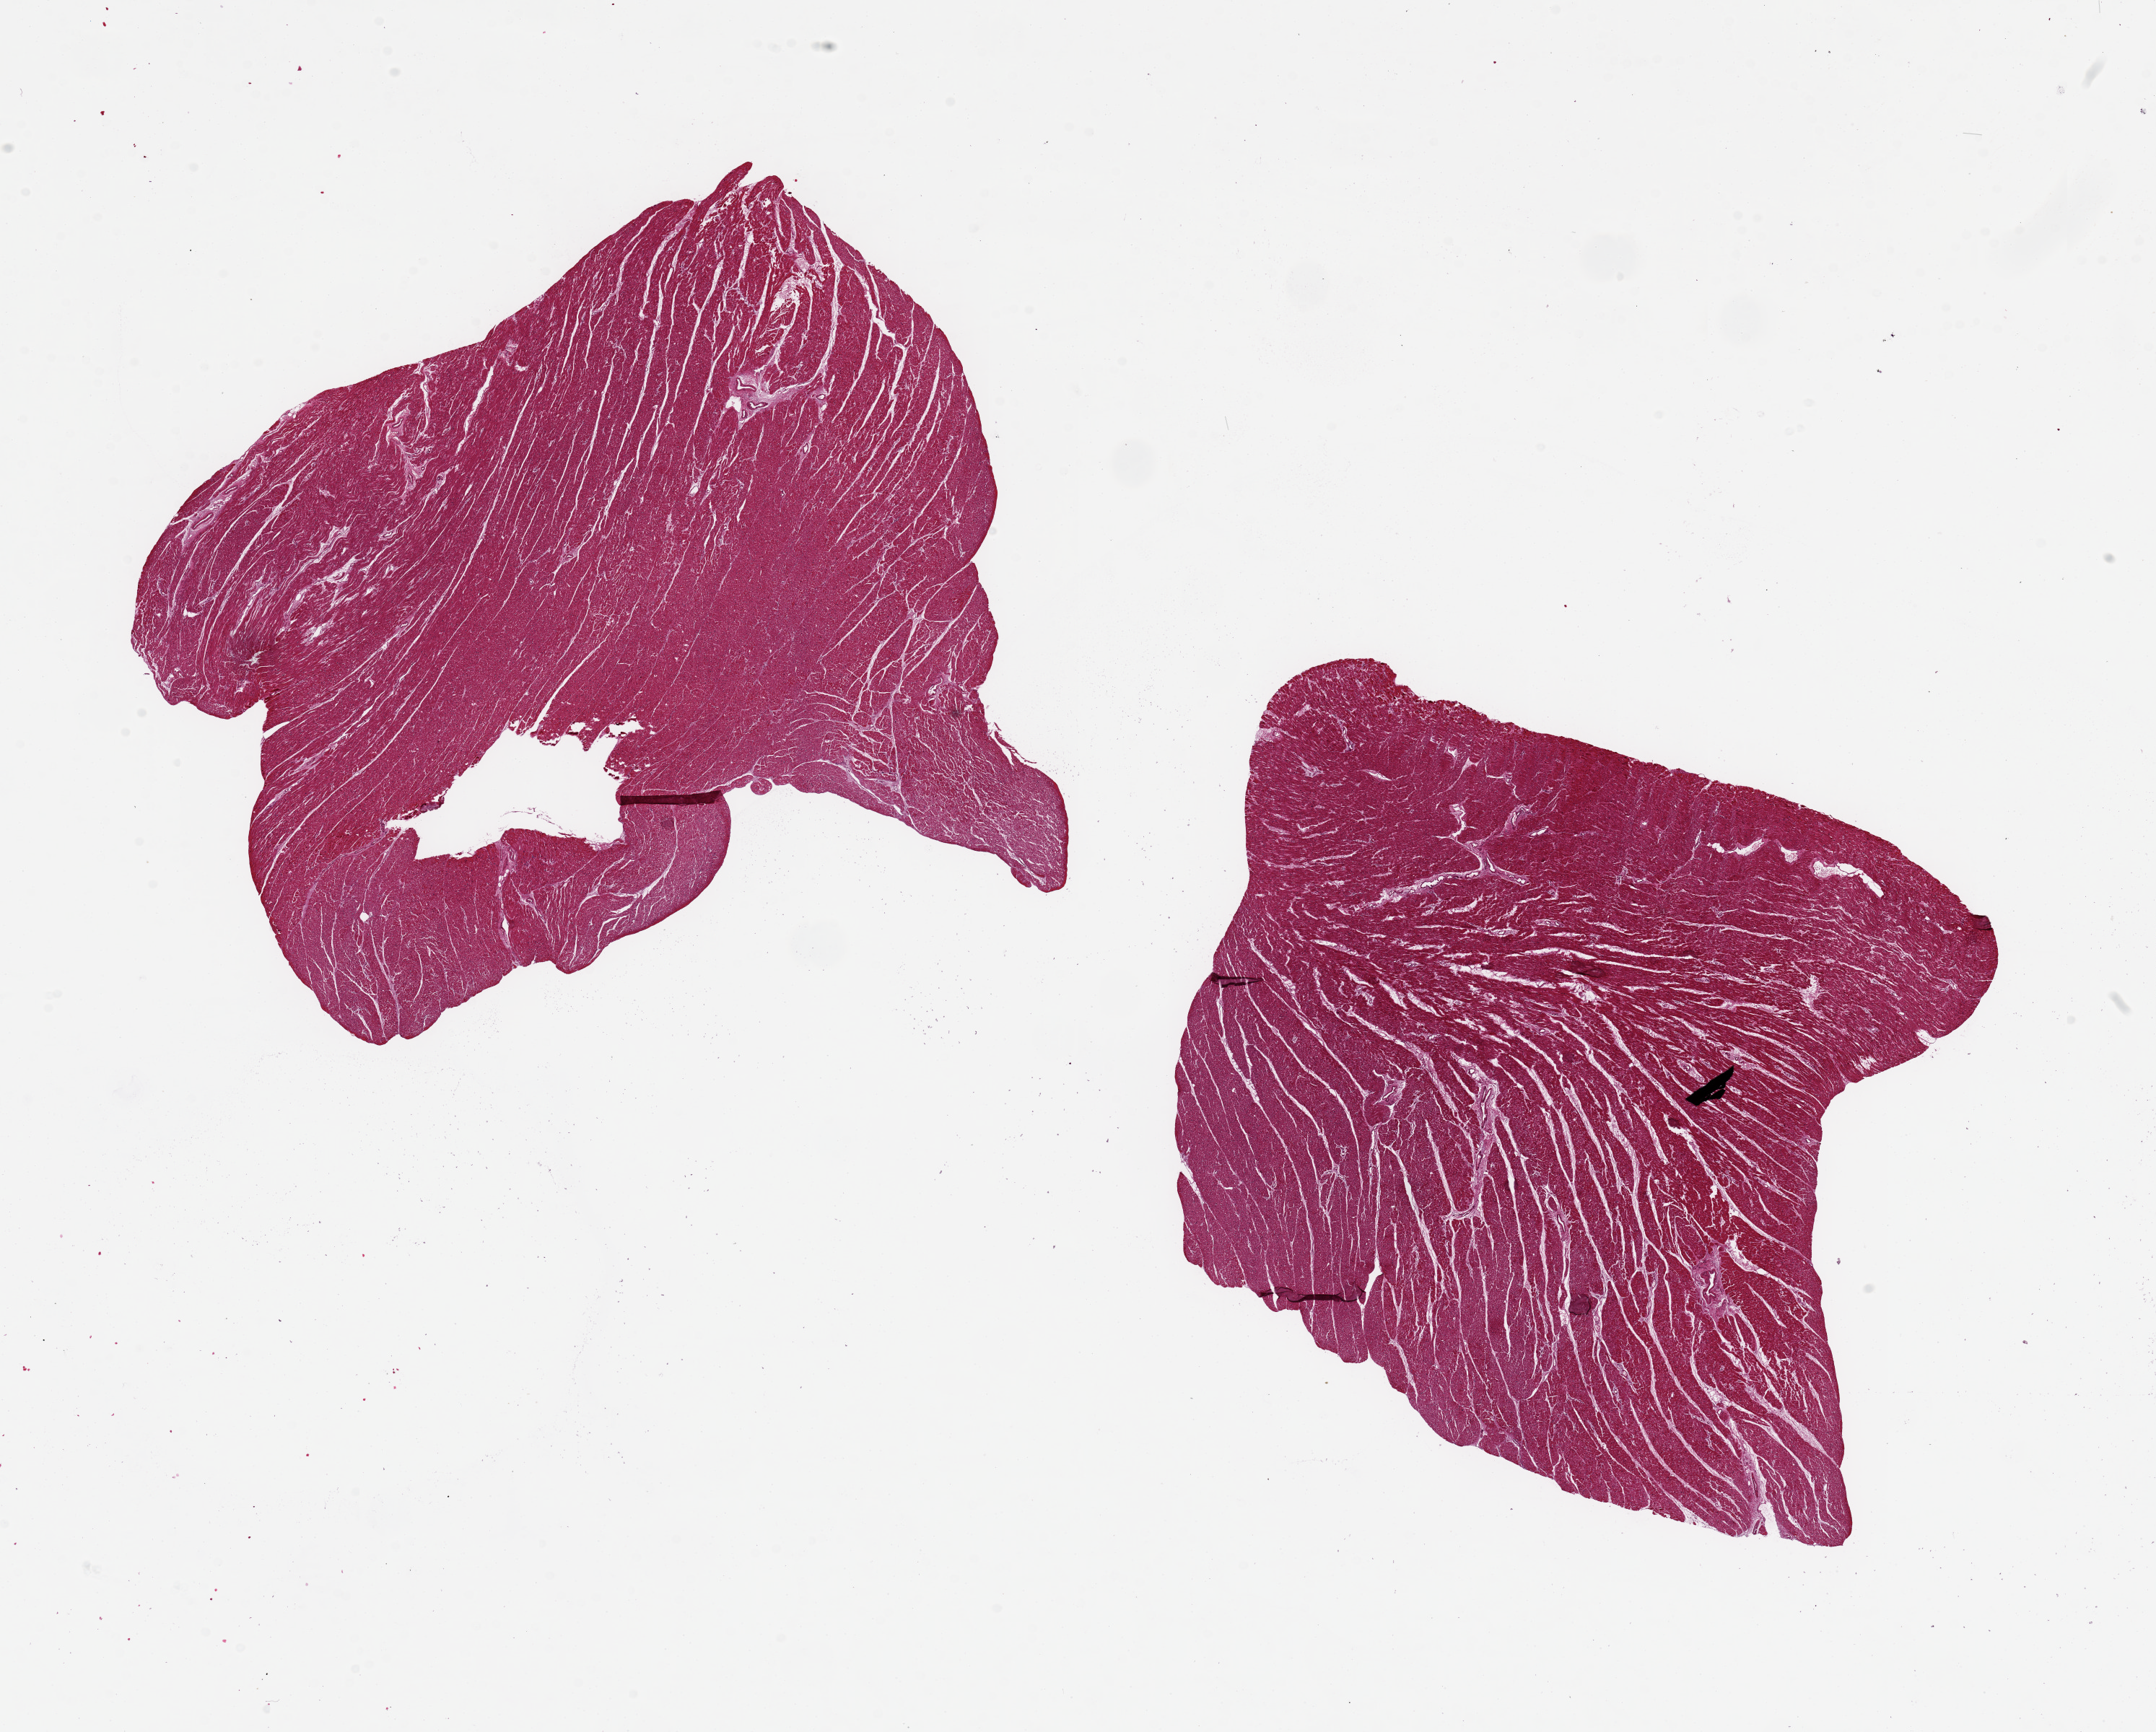
Haematoxylin and eosin whole-slide image — low-resolution overview of the scanned area, about 23.6 x 19.0 mm (slide scanned at 20x); PAXgene-fixed, paraffin-embedded tissue; sampled site (target tissue): heart; tissue donor sample. Donor sex: female.
• pathologist's review note for this sample: 2 pieces, 9x6 & 8x8mm; no adipose